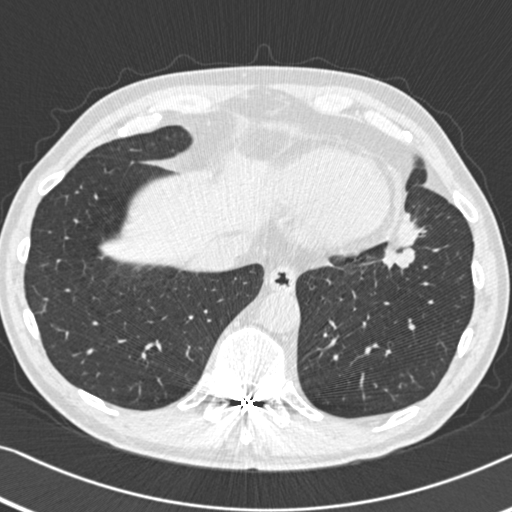
Low-dose screening chest CT, one axial slice; position 123 of 383 along the scan axis; reconstruction kernel B30f; 120 kVp; lung window (W 1500 / L -600 HU); 1 mm slice thickness; 512 × 512 image matrix, field of view 332 × 332 mm.
Structures marked on this image (manually delineated by an expert):
- lesion 1 (tumor, upper lobe of left lung): bounding box (x1, y1, x2, y2) in pixels: (383, 214, 425, 268)